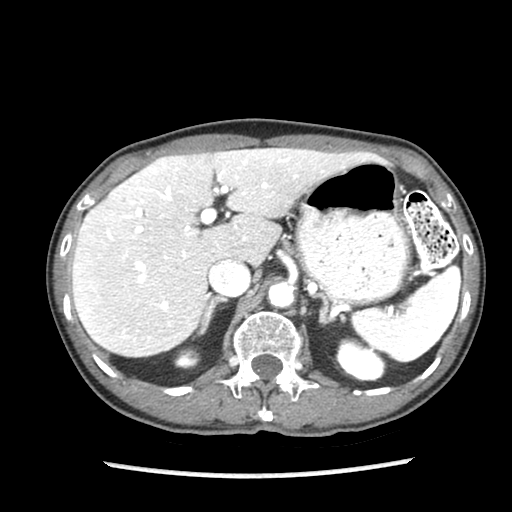
Contrast-enhanced abdominal CT (liver protocol), one axial slice. Position 57 of 87 along the scan axis. Reconstruction kernel STANDARD. 140 kVp. Soft-tissue window (W 400 / L 40 HU). 512 × 512 image matrix, field of view 300 × 300 mm. Case-level facts recorded for this patient, not image findings: diagnosis: hepatocellular carcinoma (patient treated with transarterial chemoembolisation; whether this scan precedes or follows treatment is not stated here); TNM stage (as recorded): Stage-IIIB; Child-Pugh class: A; tumour nodularity: uninodular.
Annotated regions visible in this slice (semi-automatically segmented with operator editing):
- liver parenchyma outside the tumour (the mass and vessels are separate outlines, so this box may not span the whole liver): bounding box [x1, y1, x2, y2] px = [72, 148, 370, 356]
- liver vessels: [83, 158, 296, 320]